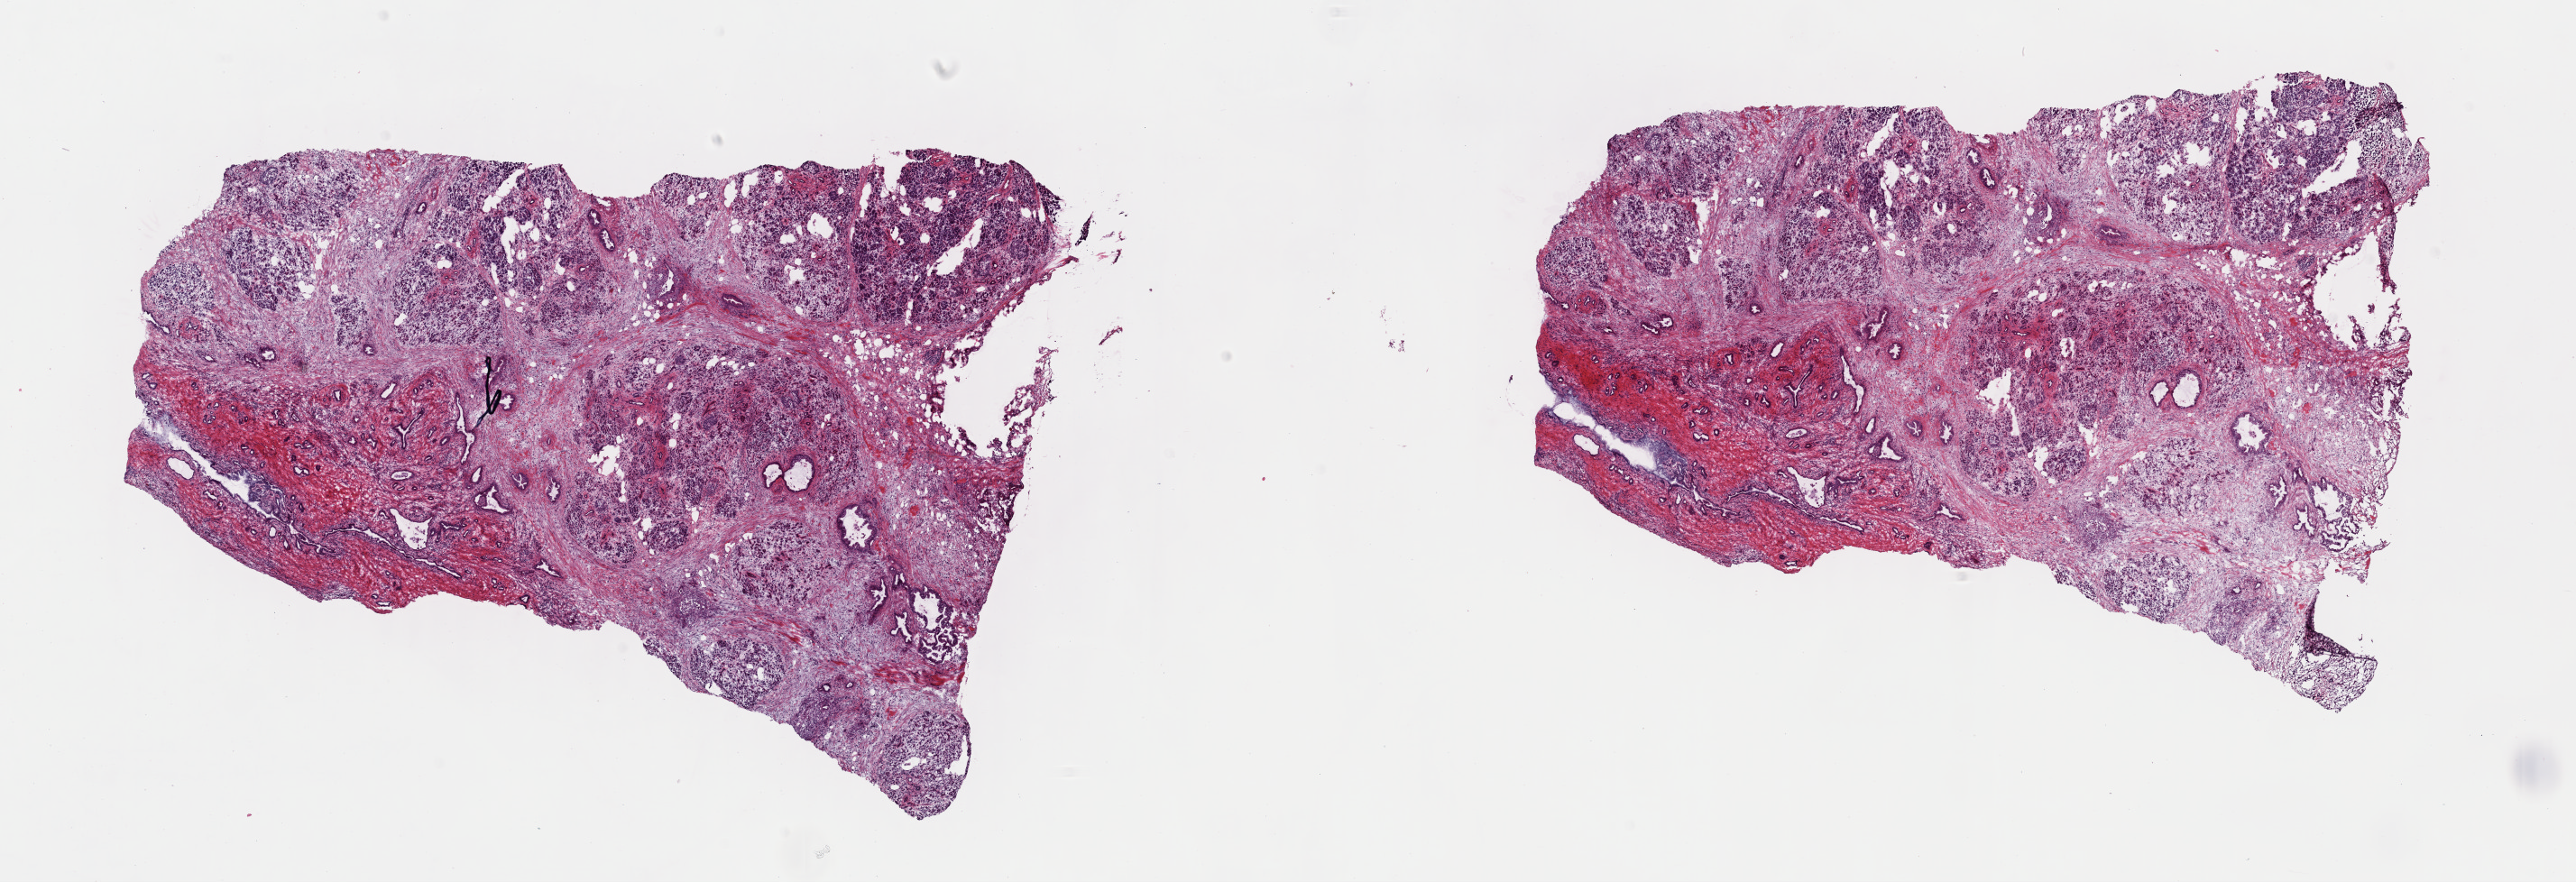
Digitized H&E-stained tissue section (whole slide) — whole scanned area (about 22.6 x 7.7 mm, acquisition: 40x scan) shown as a low-resolution overview. Frozen section from the top of the tissue portion. Sample: primary tumour, pancreas. Female patient; age at initial diagnosis 58 years. Histologic grade: G2 (moderately differentiated). Composition of this section per pathologist review: tumour cells 75%, tumour nuclei 65%, normal cells 25%, stromal cells 0%, necrosis 0%. Inflammatory infiltration, as recorded: lymphocyte infiltration 2%, monocyte infiltration 0%, neutrophil infiltration 0%.
AJCC pathologic stage: IIB. Histologic diagnosis: Infiltrating duct carcinoma, NOS (head of pancreas).